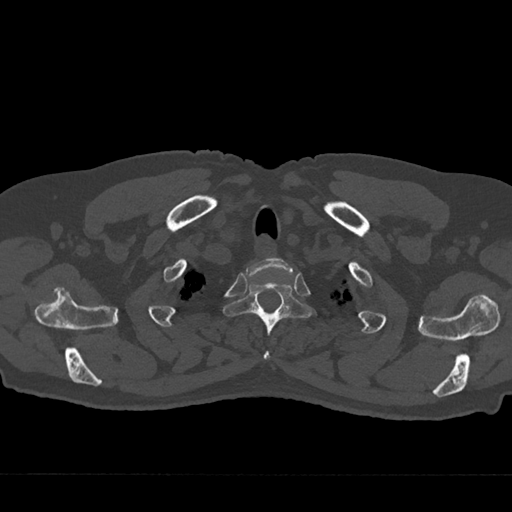
CT including the spine, one axial slice. Position 623 of 797 along the scan axis. Bone window (W 1800 / L 400 HU). 0.5 mm slice thickness. 512 × 512 image matrix, field of view 377 × 377 mm. Male patient, age 75 years. Case-level facts recorded for this patient, not image findings: primary cancer: renal.
Annotated regions visible in this slice (semi-automatic segmentation, software-assisted and operator-edited):
- T1 vertebra: bounding box <246,258,294,278> (left, top, right, bottom; pixels)
- T2 vertebra: <222,281,314,360>